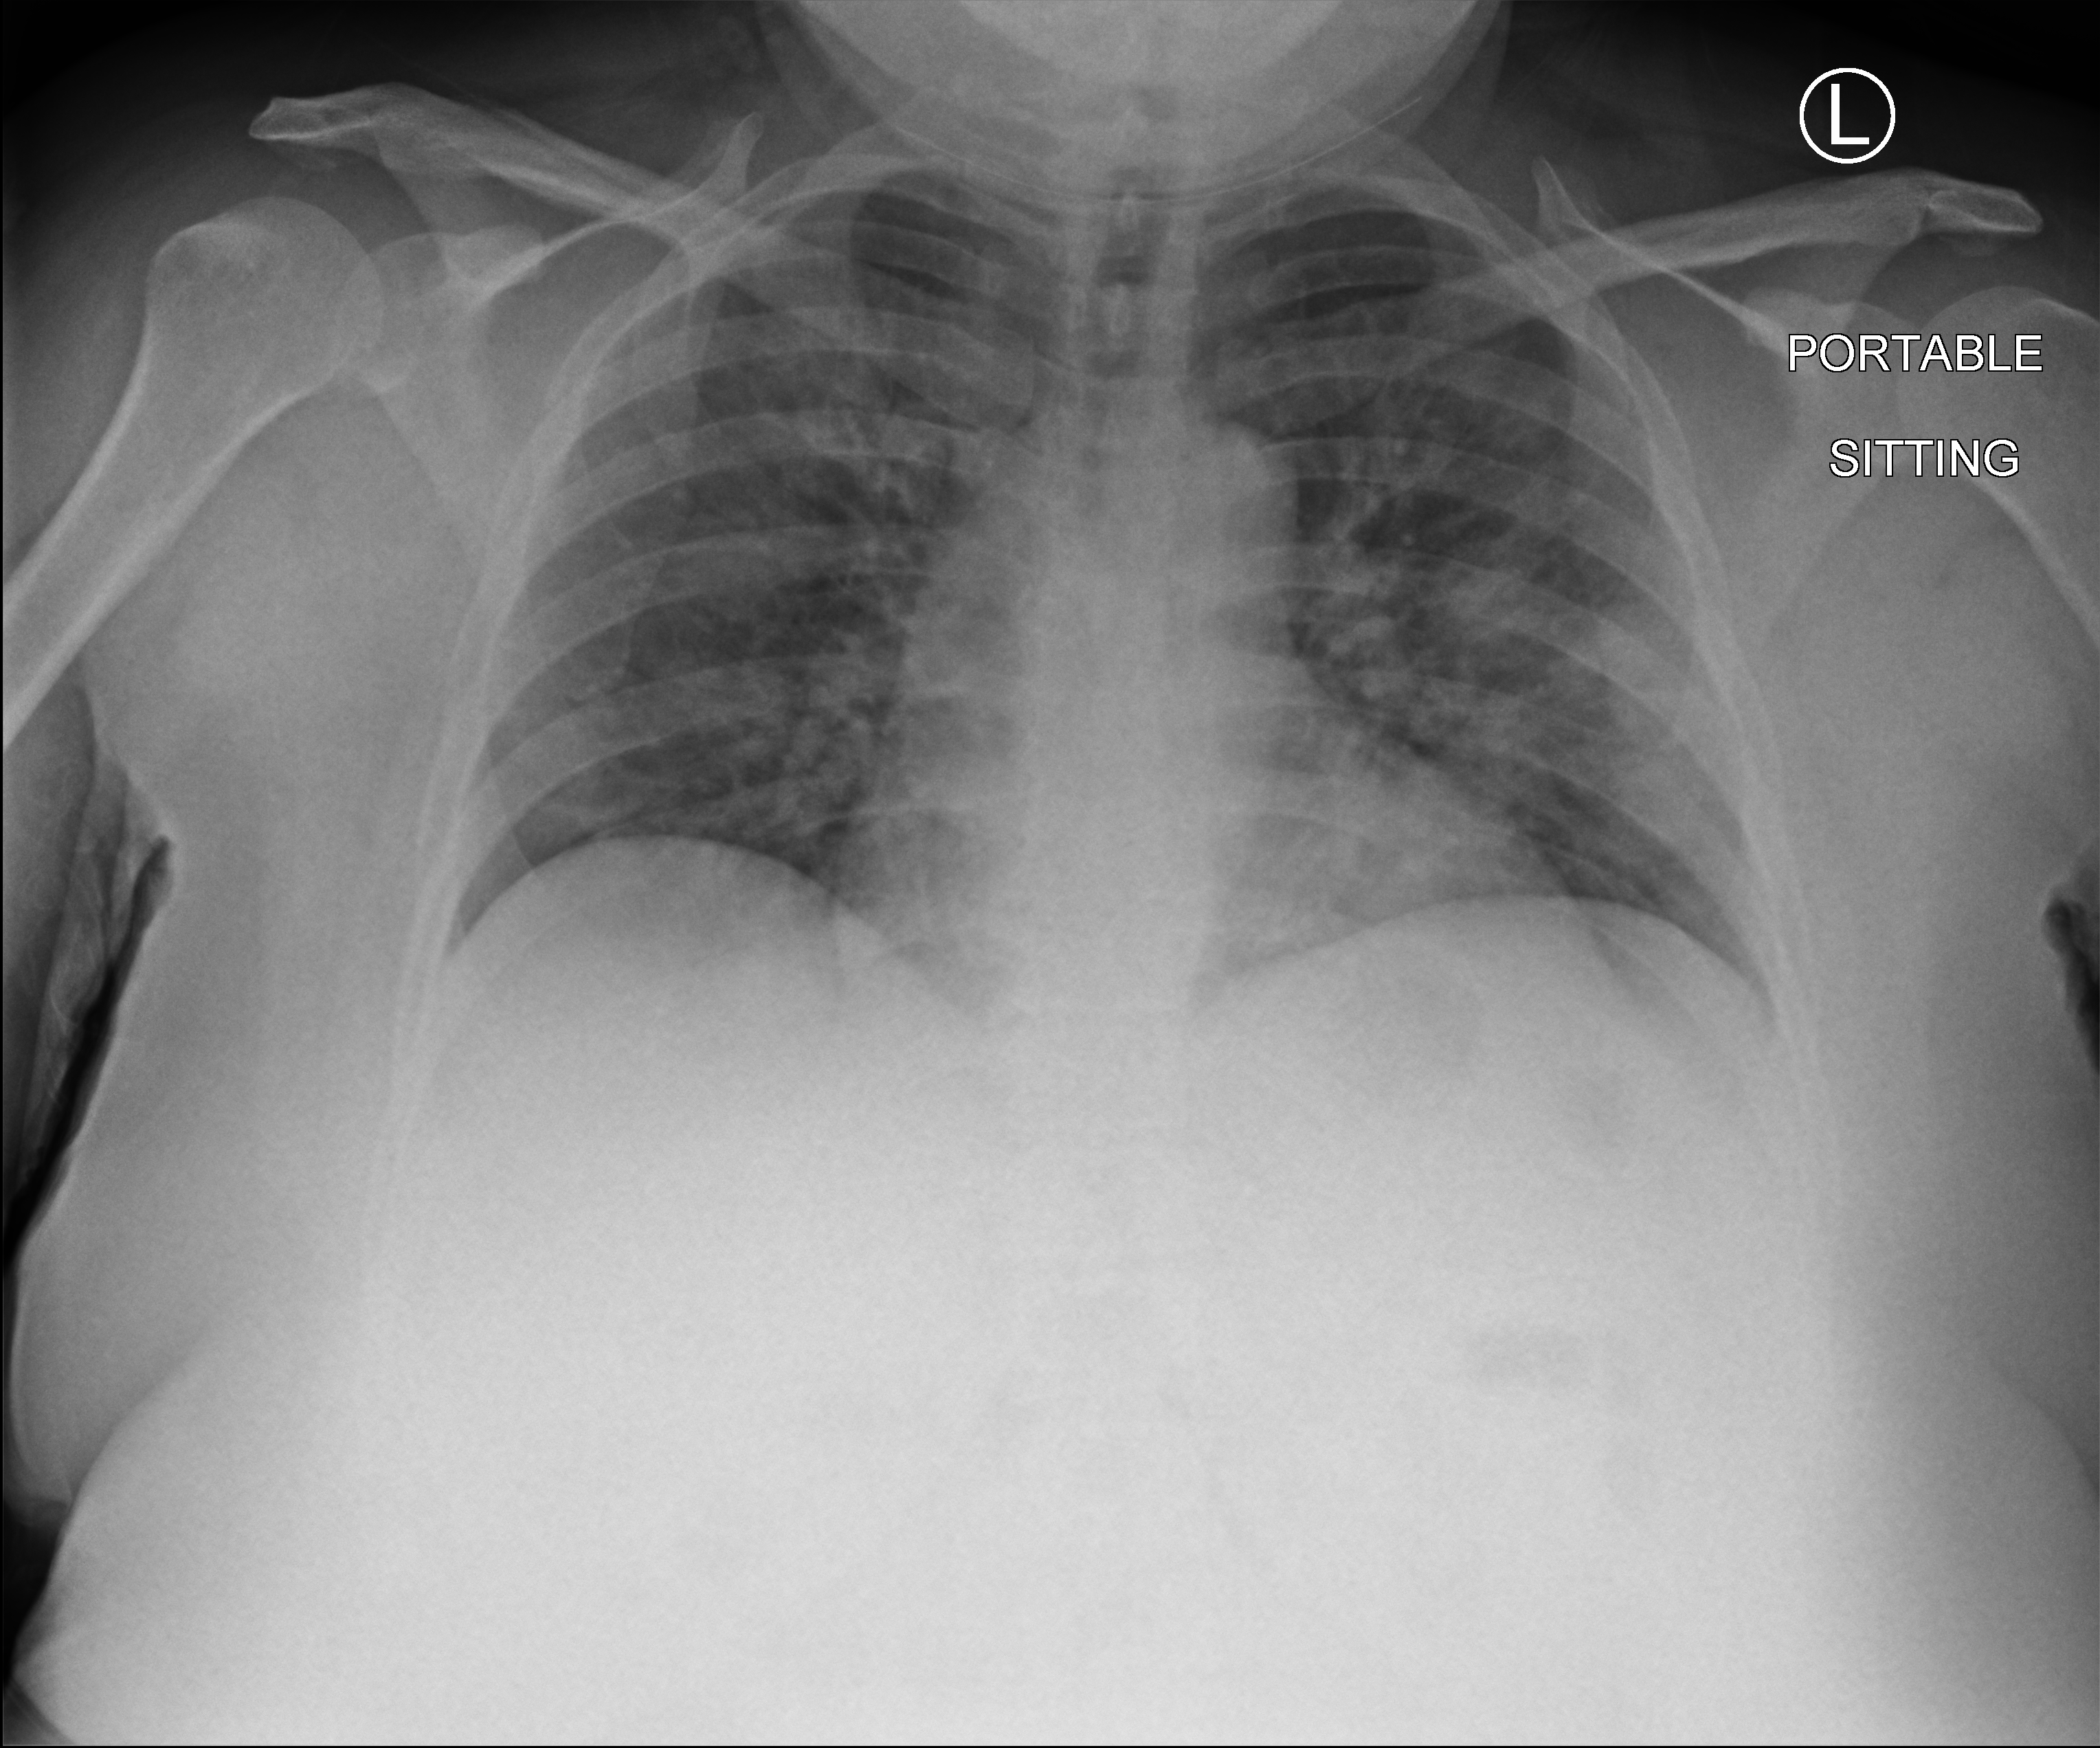
Bedside chest radiograph (computed radiography), anteroposterior (AP) projection. Female patient hospitalised with COVID-19, age 18–59 years.
Hospital-stay facts (about this admission, not read from this image; timing relative to this image not recorded): admitted to intensive care during this hospital stay: no; hypertension (admission record): yes; length of hospital stay: 1 day.